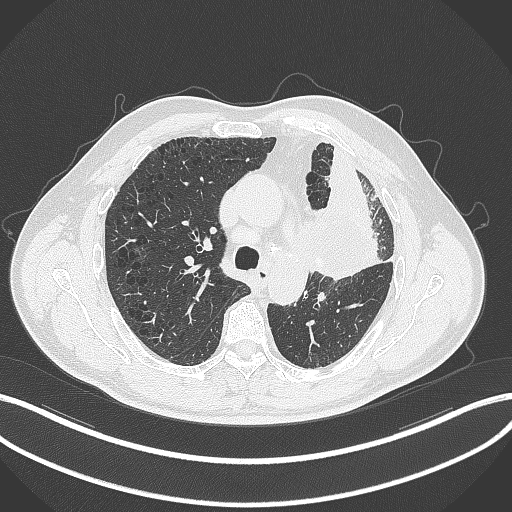
Chest CT, one axial slice. Slice 209 of 297 in the series (ordered by position). Reconstruction kernel B70f. 120 kVp. Lung window (W 1500 / L -600 HU). 1 mm slice thickness. 512 × 512 image matrix, field of view 400 × 400 mm. Male patient, age 68 years. Case-level facts recorded for this patient, not image findings: clinical TNM (as recorded): T3 N3 M1.
Outlined on this slice (bounding box drawn by a radiologist):
- lung tumour (recorded histology: adenocarcinoma): bounding box [x1, y1, x2, y2] px = [315, 187, 385, 282]